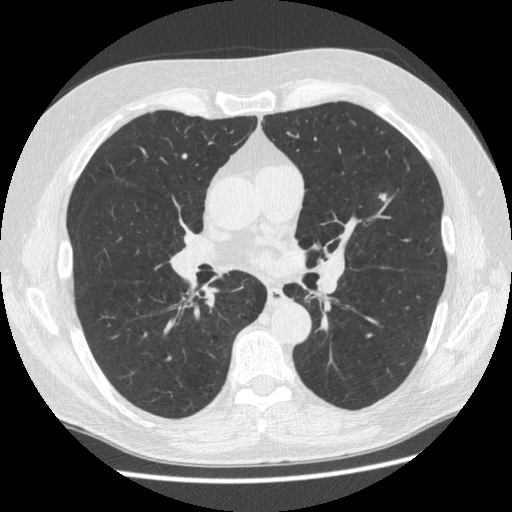
Low-dose screening chest CT, one axial slice; position 300 of 545 along the scan axis; 120 kVp; lung window (W 1500 / L -600 HU); 1.25 mm slice thickness; 512 × 512 image matrix.
Outlined on this slice (outlined manually by an expert reader):
- lesion 1 (nodule, upper lobe of left lung): box from (x=379, y=194) to (x=386, y=201) px